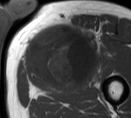
MRI of an extremity soft-tissue mass, one axial slice. Position 46 of 55 along the scan axis. MR volume resampled by the dataset authors to the PET/CT grid (not the native acquisition matrix). 3.27 mm slice thickness. 131 × 118 image matrix, field of view 128 × 115 mm. Male patient. Case-level facts recorded for this patient, not image findings: histological type: pleiomorphic liposarcoma; grade: high; site of the primary tumour: left thigh.
Outlined on this slice (expert contour drawn on MRI and transferred to this co-registered scan by the dataset authors):
- gross tumour volume including surrounding oedema: box from (x=27, y=20) to (x=99, y=83) px
- gross tumour volume (mass): (x=27, y=29)–(x=92, y=83)